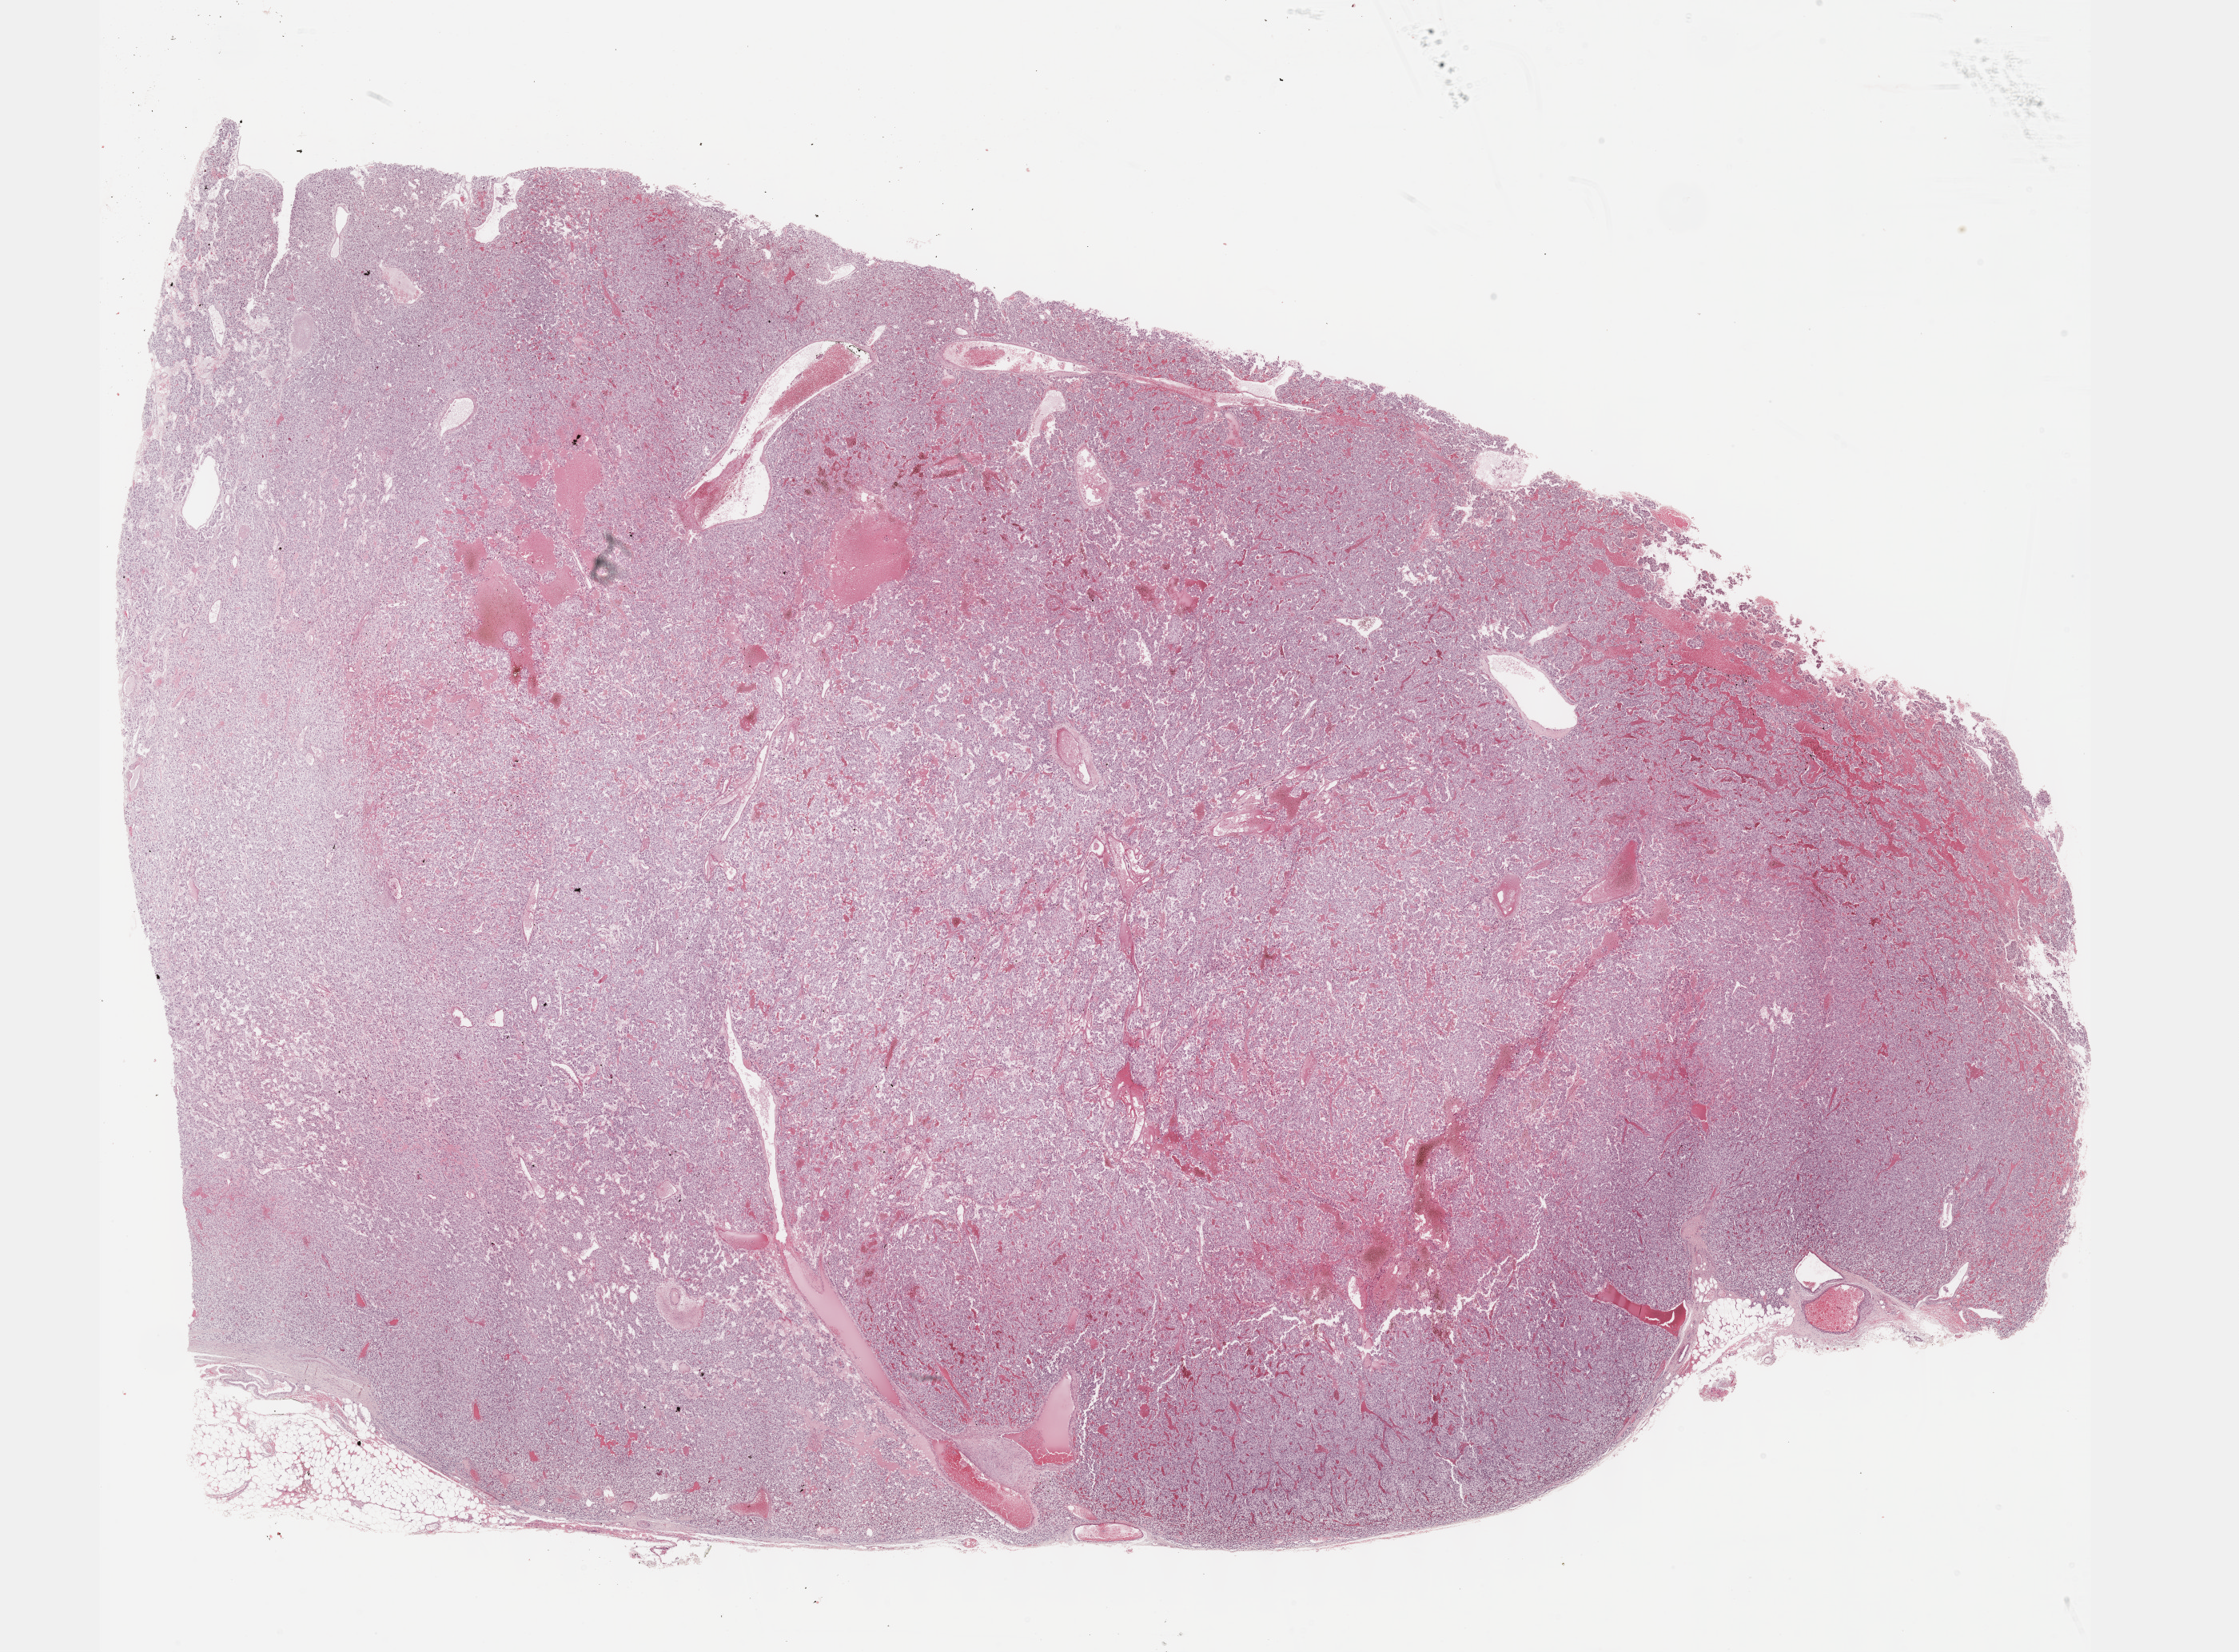
H&E-stained whole-slide image, shown as a low-resolution overview of the whole scanned area (about 22.6 x 16.7 mm, slide scanned at 40x). FFPE section. Sample: primary tumour, adrenal gland. Female, age 73 years at initial diagnosis.
Histologic diagnosis: Pheochromocytoma, malignant.